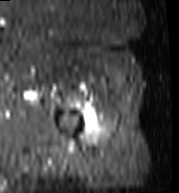
MRI of an extremity soft-tissue mass, one axial slice. Position 98 of 103 along the scan axis. STIR. MR volume resampled by the dataset authors to the PET/CT grid (not the native acquisition matrix). 3.27 mm slice thickness. 179 × 193 image matrix, field of view 175 × 188 mm. Female patient. From the clinical record (not read from this slice): histological type: undifferentiated – high grade; grade: high; site of the primary tumour: left thigh.
Outlined on this slice (expert contour drawn on MRI and transferred to this co-registered scan by the dataset authors):
- gross tumour volume including surrounding oedema: bounding box (x1, y1, x2, y2) in pixels: (91, 124, 96, 129)